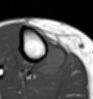
MRI of an extremity soft-tissue mass, one axial slice. Slice 27 of 54 in the series (ordered by position). MR volume resampled by the dataset authors to the PET/CT grid (not the native acquisition matrix). 3.27 mm slice thickness. 93 × 99 image matrix. Female patient. Case-level facts recorded for this patient, not image findings: histological type: undifferentiated – high grade; grade: high; site of the primary tumour: right thigh.
Outlined on this slice (expert contour drawn on MRI and transferred to this co-registered scan by the dataset authors):
- gross tumour volume (mass): bounding box (x1, y1, x2, y2) in pixels: (36, 36, 66, 74)